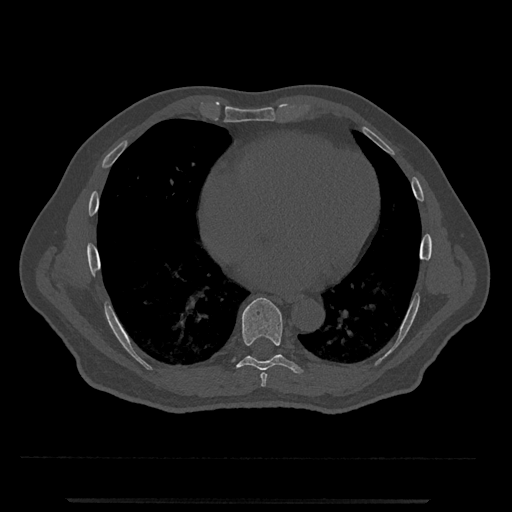
CT including the spine, one axial slice; slice 627 of 797 in the series (ordered by position); reconstruction kernel Br40s/3; bone window (W 1800 / L 400 HU); 512 × 512 image matrix. Male patient, age 63 years. Case-level facts recorded for this patient, not image findings: primary cancer: prostate.
Structures marked on this image (semi-automatically segmented with operator editing):
- T7 vertebra: bounding box [x1, y1, x2, y2] px = [260, 372, 267, 387]
- T8 vertebra: [233, 298, 304, 374]